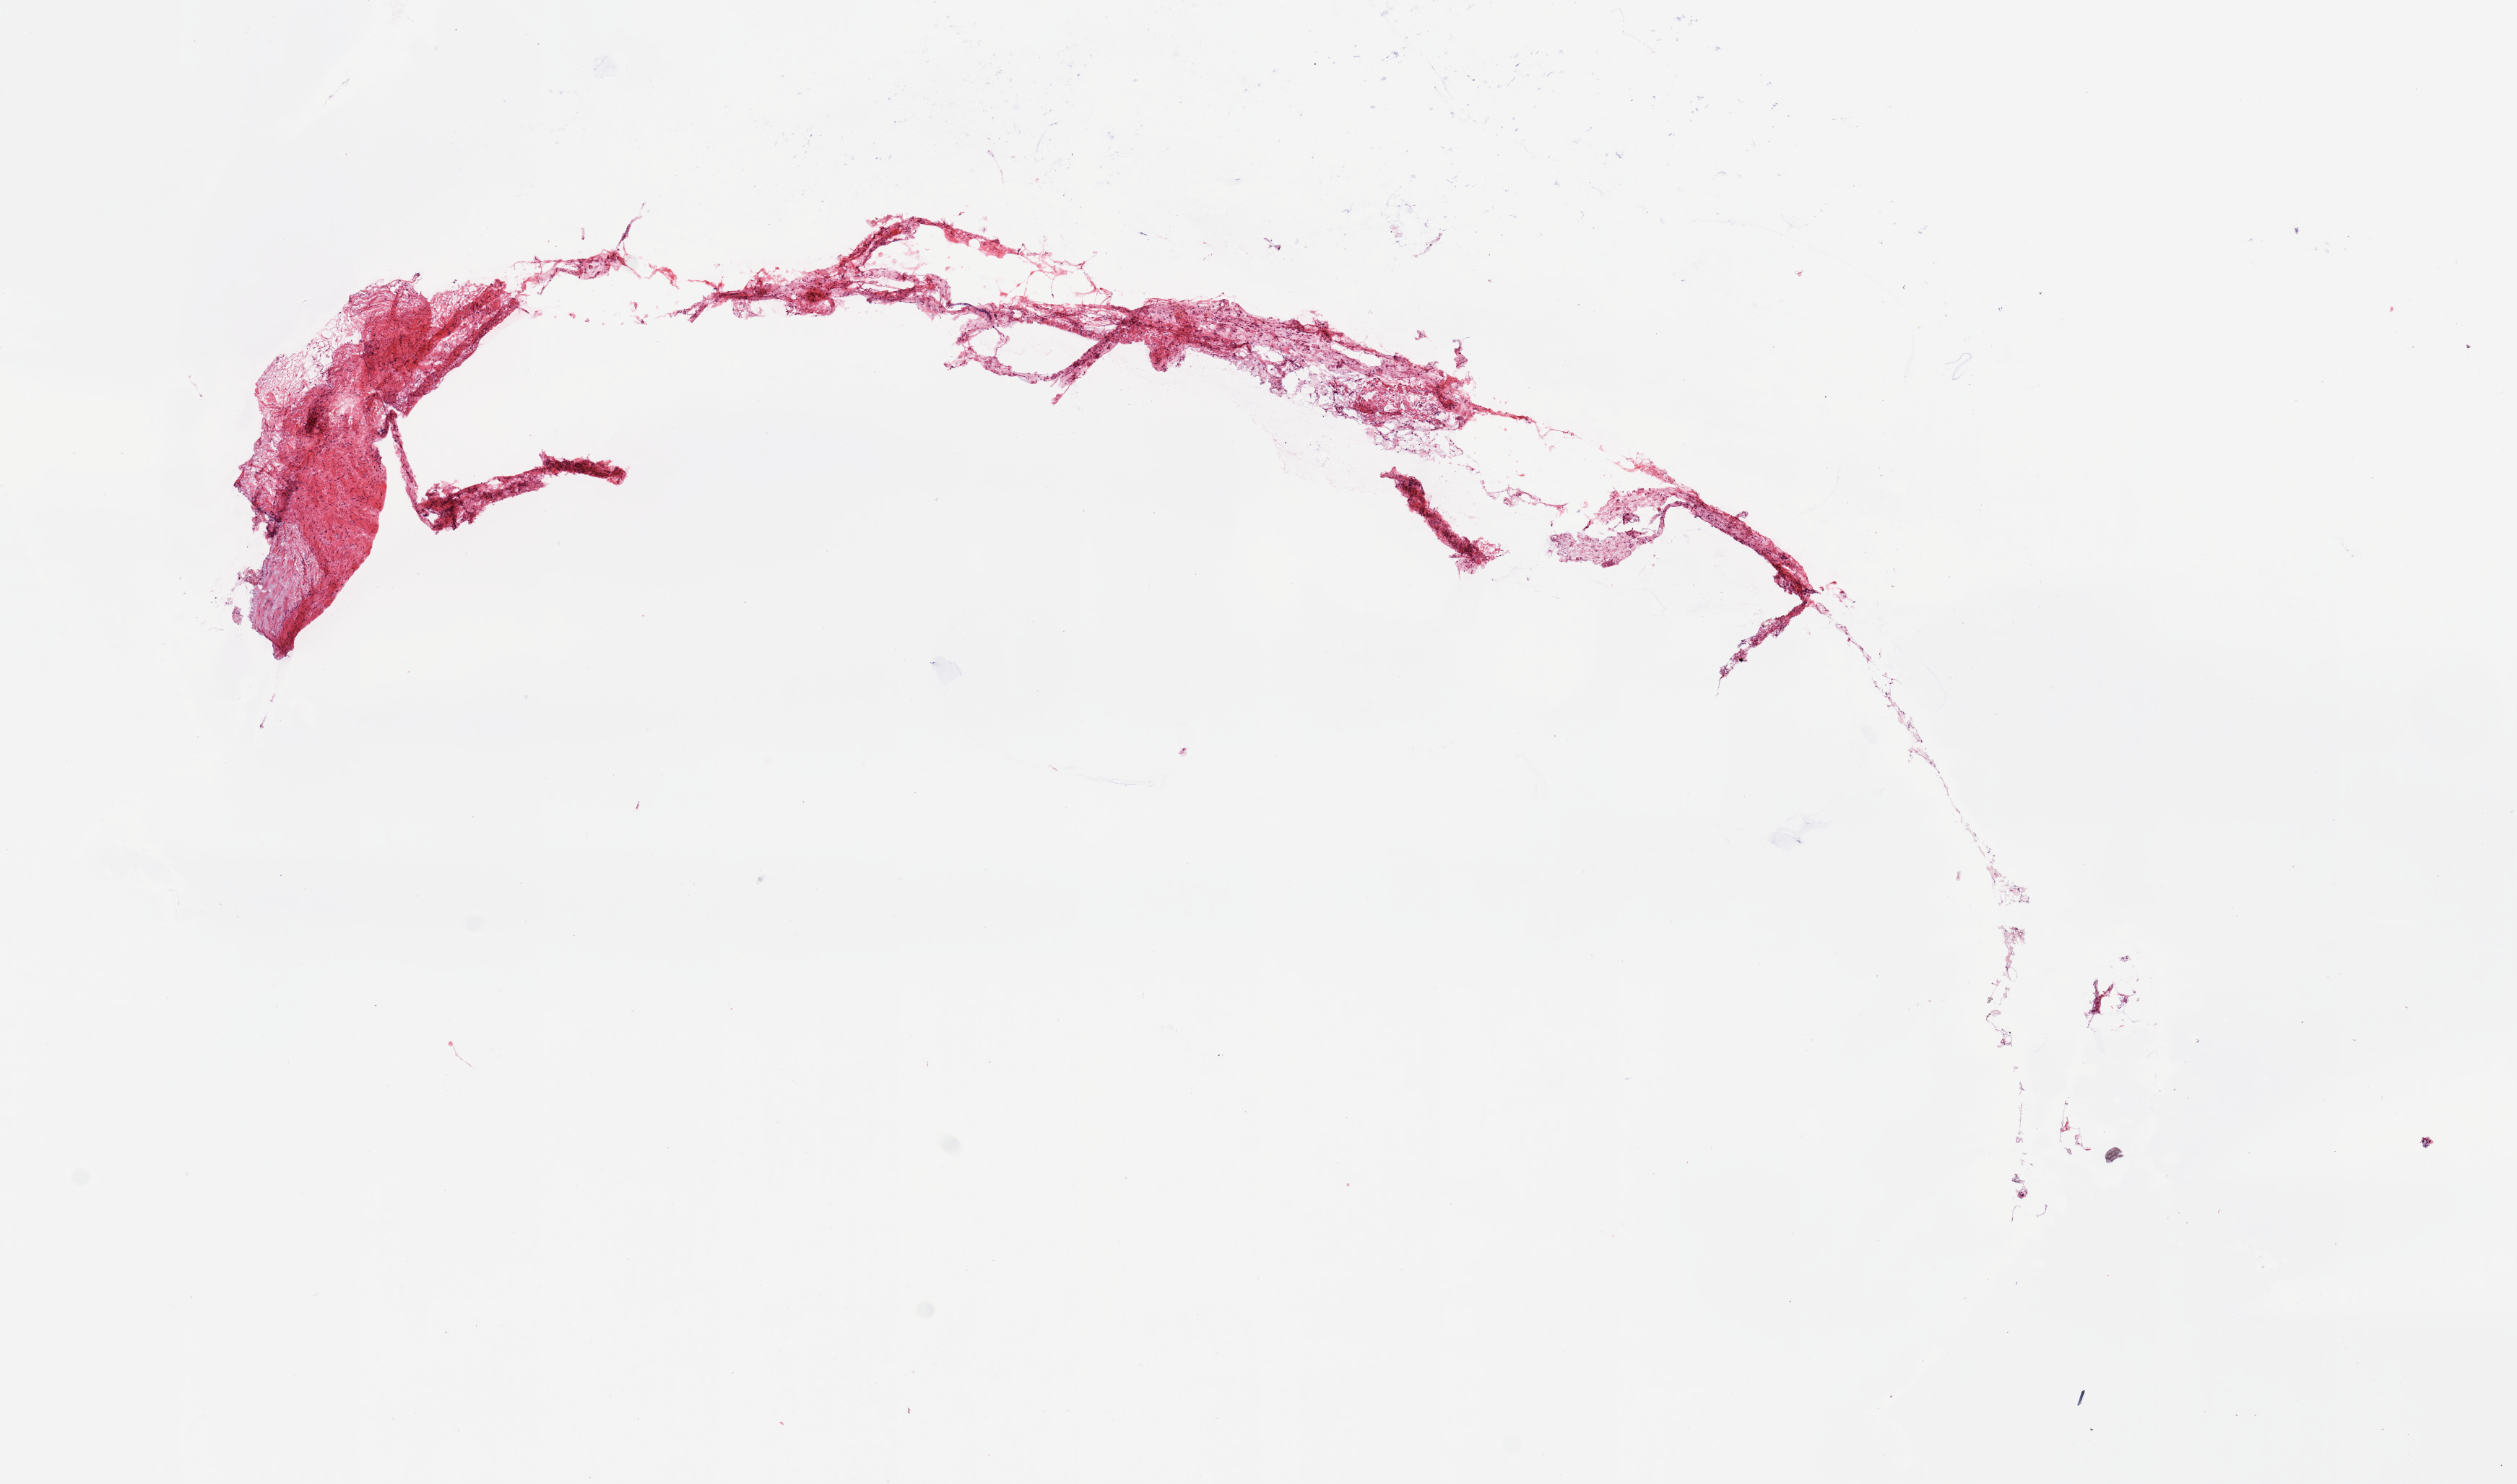
Whole-slide histology image, Hematoxylin and eosin (H&E) stained, whole scanned area (about 13.8 x 8.1 mm, acquisition: 20x scan) shown as a low-resolution overview. Normal (non-tumour) tissue sample, pancreas. Female, 59 y/o.
This section: normal (non-tumour) tissue from the same patient. Patient diagnosis: Infiltrating duct carcinoma, NOS.